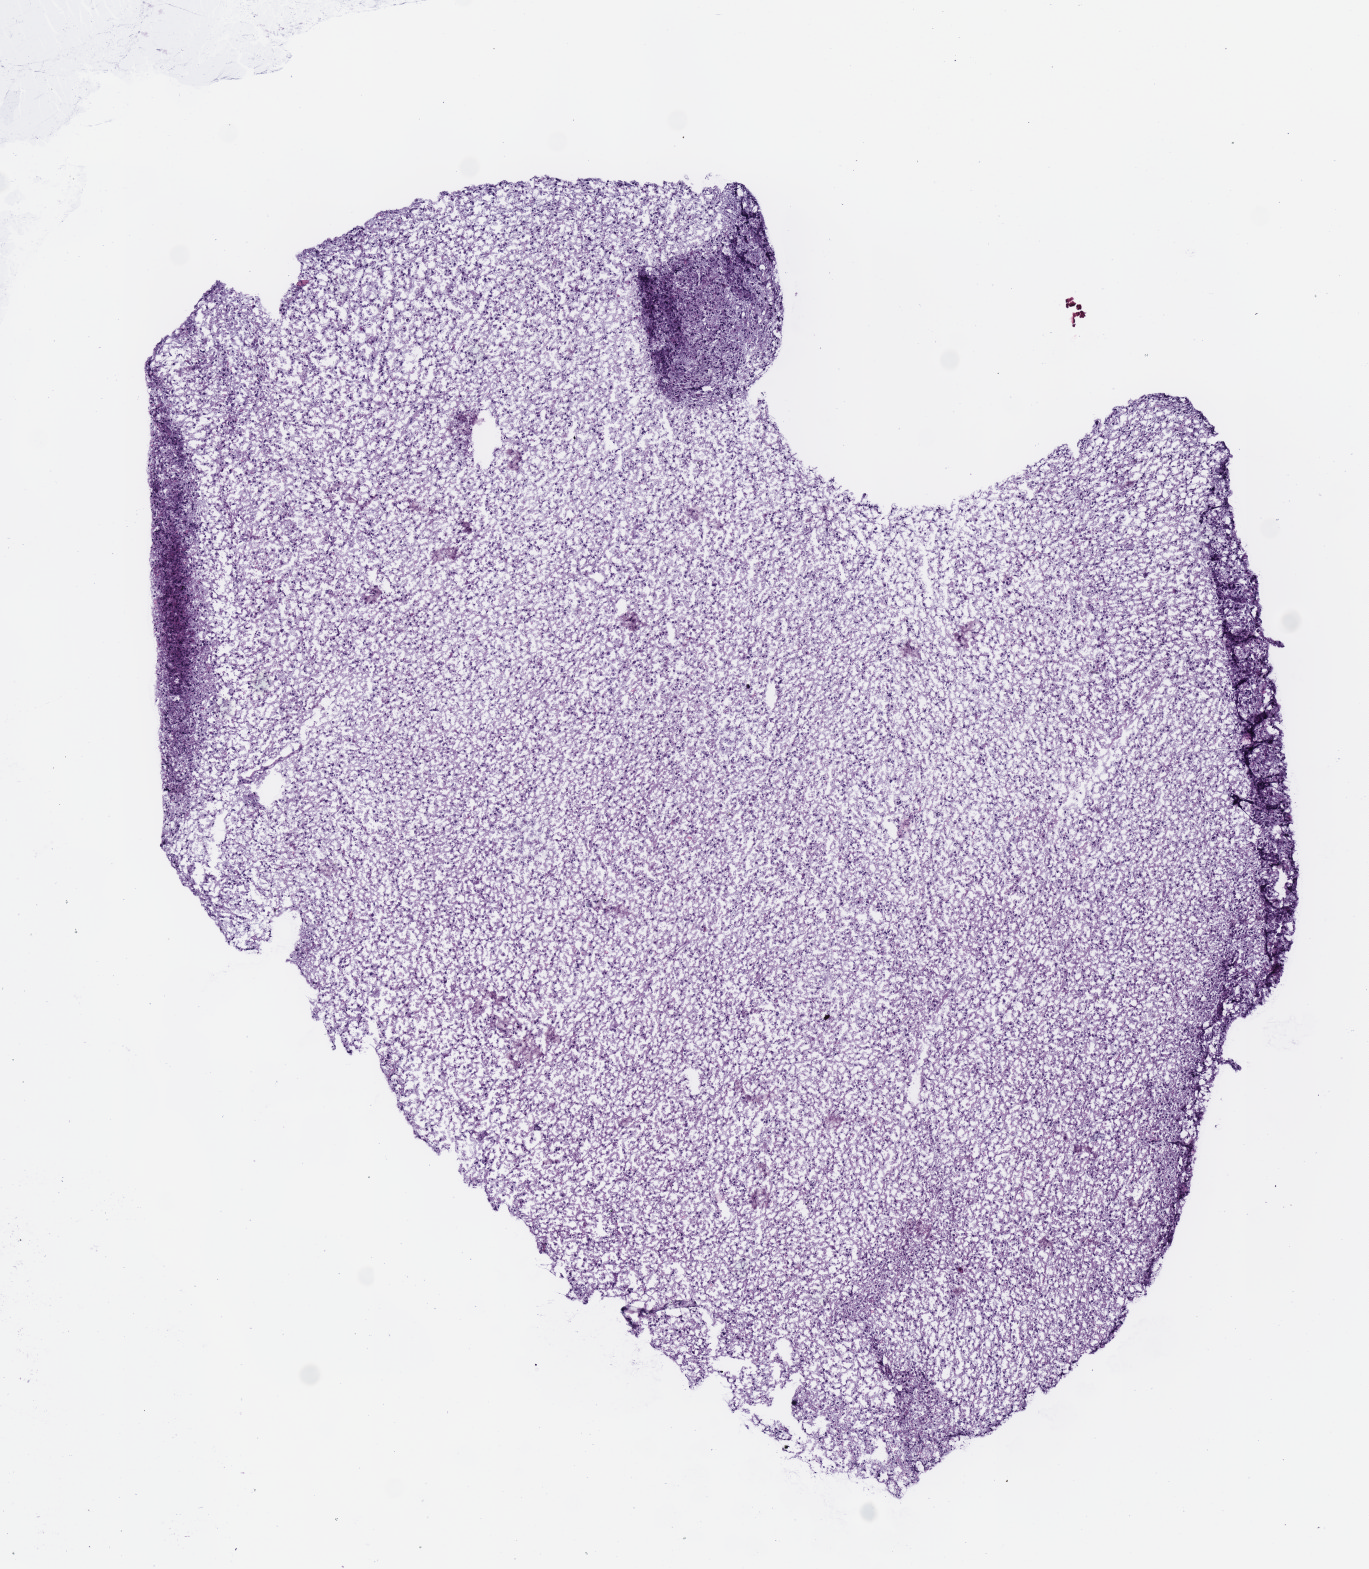
Hematoxylin and eosin (H&E) stained whole-slide image, shown as a low-resolution overview of the whole scanned area (about 5.4 x 6.2 mm, acquisition: 40x scan), frozen section from the top of the tissue portion, primary tumour sample from the brain. Female, age 37 years at initial diagnosis. Histologic grade: G2 (moderately differentiated). Slide review estimates, as recorded: tumour cells 100%, tumour nuclei 70%, normal cells 0%, stromal cells 0%, necrosis 0%.
Pathologic diagnosis: Mixed glioma. Laterality: left.